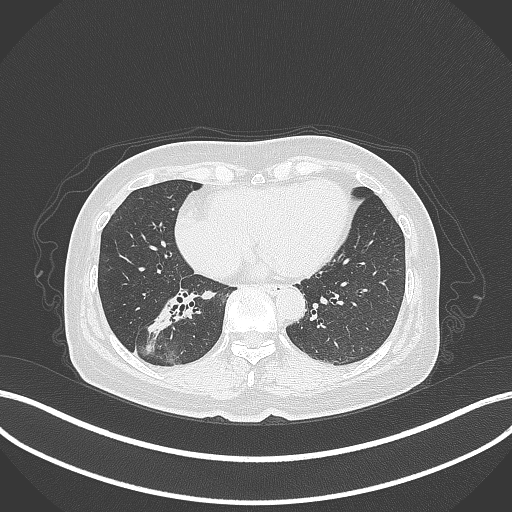
Chest CT, one axial slice. Position 145 of 429 along the scan axis. Reconstruction kernel B70f. 120 kVp. Lung window (W 1500 / L -600 HU). 512 × 512 image matrix. Female patient, age 67 years. Case-level facts recorded for this patient, not image findings: clinical TNM (as recorded): T1c N1 M0; histopathological grade: G2-3.
Structures marked on this image (bounding box drawn by a radiologist):
- lung tumour (recorded histology: adenocarcinoma): box from (x=143, y=291) to (x=196, y=341) px